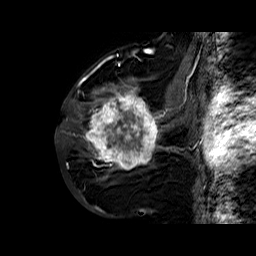
Breast MRI (dynamic contrast-enhanced), one sagittal slice. Position 30 of 60 along the scan axis. Dynamic contrast-enhanced series, time point 2 of 6 at this slice position (early post-contrast). 1.5 T. TE 6.4 ms, TR 32.8 ms. 4 mm slice thickness. 256 × 256 image matrix. Female patient. From the clinical record (not read from this slice): setting: breast cancer imaged before/during neoadjuvant chemotherapy; receptor status: HR-positive, HER2-negative.
Outlined on this slice (semi-automatically segmented with operator editing):
- analysis volume of interest (the breast-tissue region the enhancement analysis was run in; not a lesion): bounding box [x1, y1, x2, y2] px = [86, 77, 163, 177]
- tumour enhancement mask (voxels above the 100 % enhancement threshold inside the analysis volume of interest): [86, 85, 163, 170]